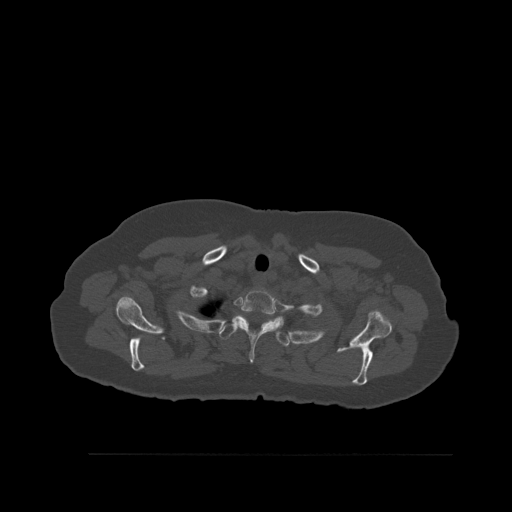
CT including the spine, one axial slice. Position 439 of 527 along the scan axis. Bone window (W 1800 / L 400 HU). 1.5 mm slice thickness. 512 × 512 image matrix. Female patient, age 73 years. Case-level facts recorded for this patient, not image findings: primary cancer: breast.
Annotated regions visible in this slice (semi-automatically segmented with operator editing):
- T1 vertebra: bounding box (x1, y1, x2, y2) in pixels: (237, 289, 280, 362)
- T2 vertebra: (219, 316, 290, 347)